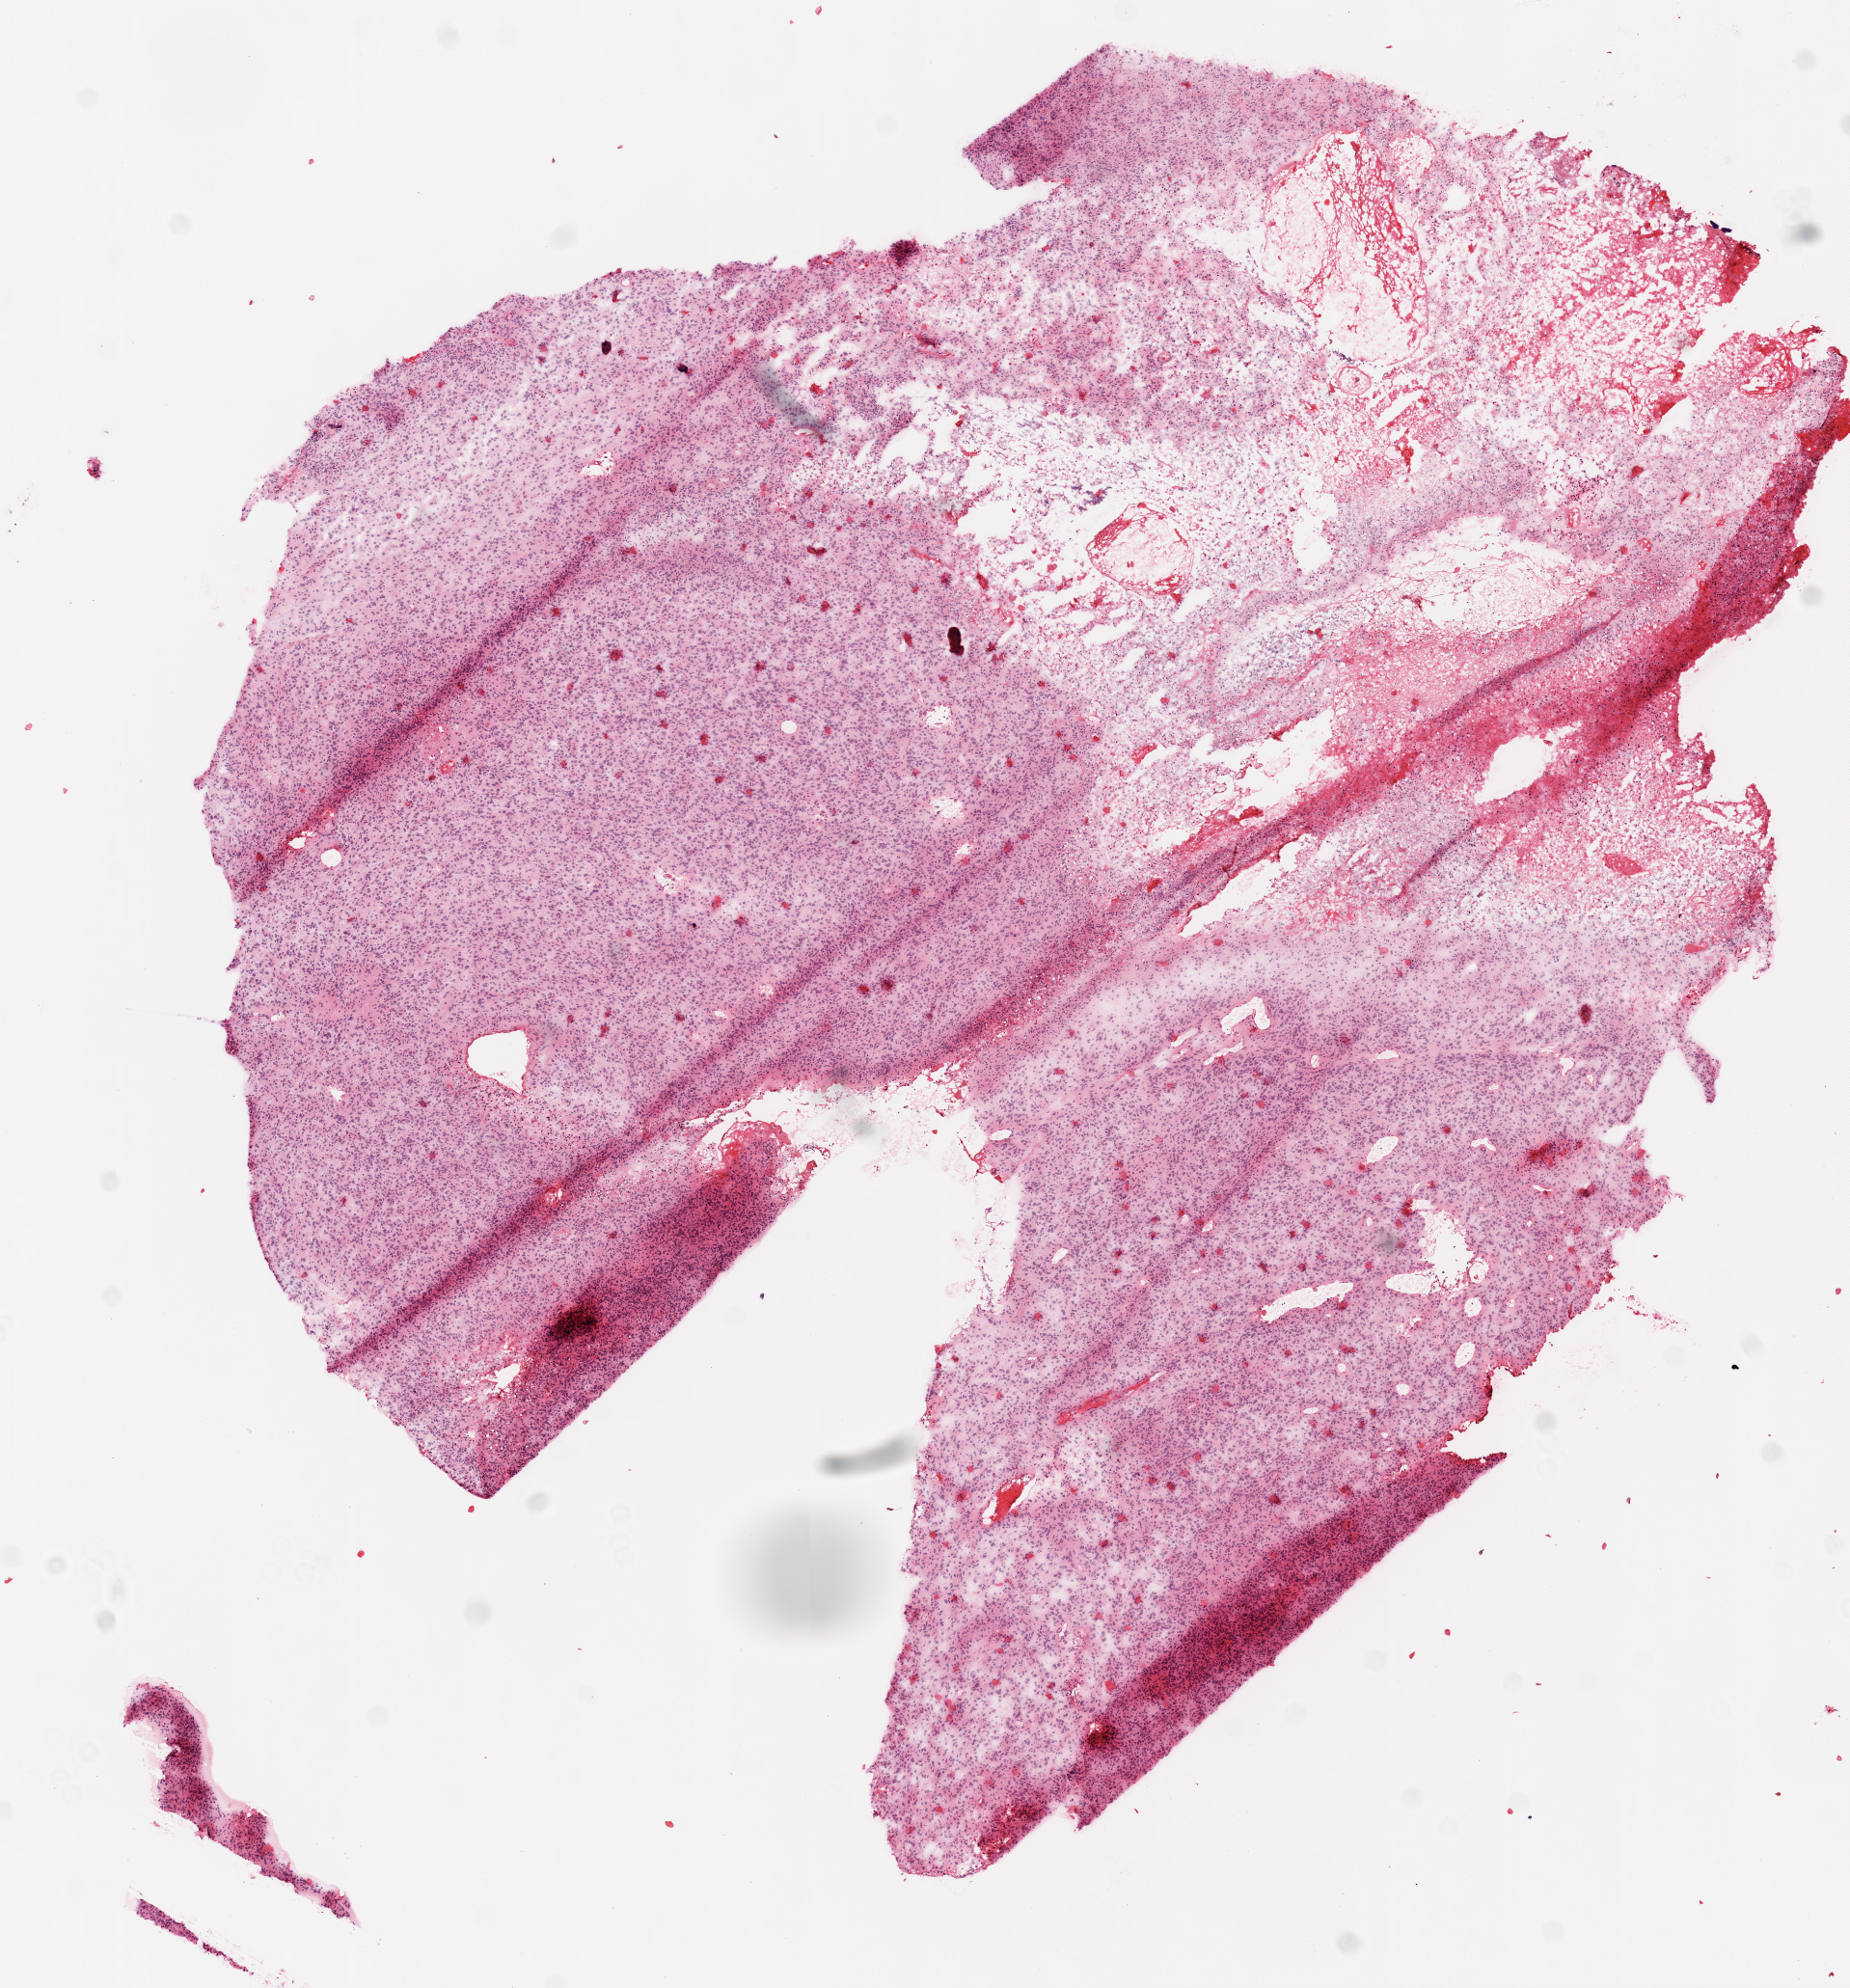
Digitized H&E tissue section (whole slide) — low-resolution overview of the scanned area, about 7.7 x 8.3 mm (slide scanned at 20x); frozen section from the bottom of the tissue portion; brain, primary tumour sample. Female, age 59 years at initial diagnosis. Pathologist review of this section (percent, as recorded): tumour cells 80%, tumour nuclei 90%, normal cells 0%, stromal cells 5%, necrosis 15%.
Diagnosis: Glioblastoma.